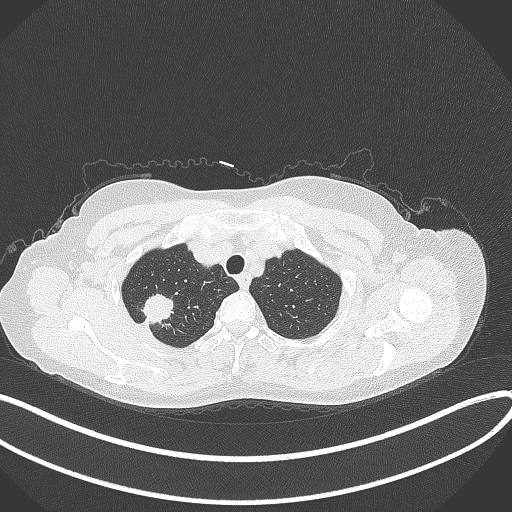
Chest CT, one axial slice; slice 314 of 337 in the series (ordered by position); lung window (W 1500 / L -600 HU); 1 mm slice thickness; 512 × 512 image matrix, field of view 400 × 400 mm. Female patient, age 50 years. Case-level facts recorded for this patient, not image findings: clinical TNM (as recorded): T1c N0 M0.
Structures marked on this image (bounding box drawn by a radiologist):
- lung tumour (recorded histology: adenocarcinoma): bounding box (x1, y1, x2, y2) in pixels: (140, 293, 176, 324)